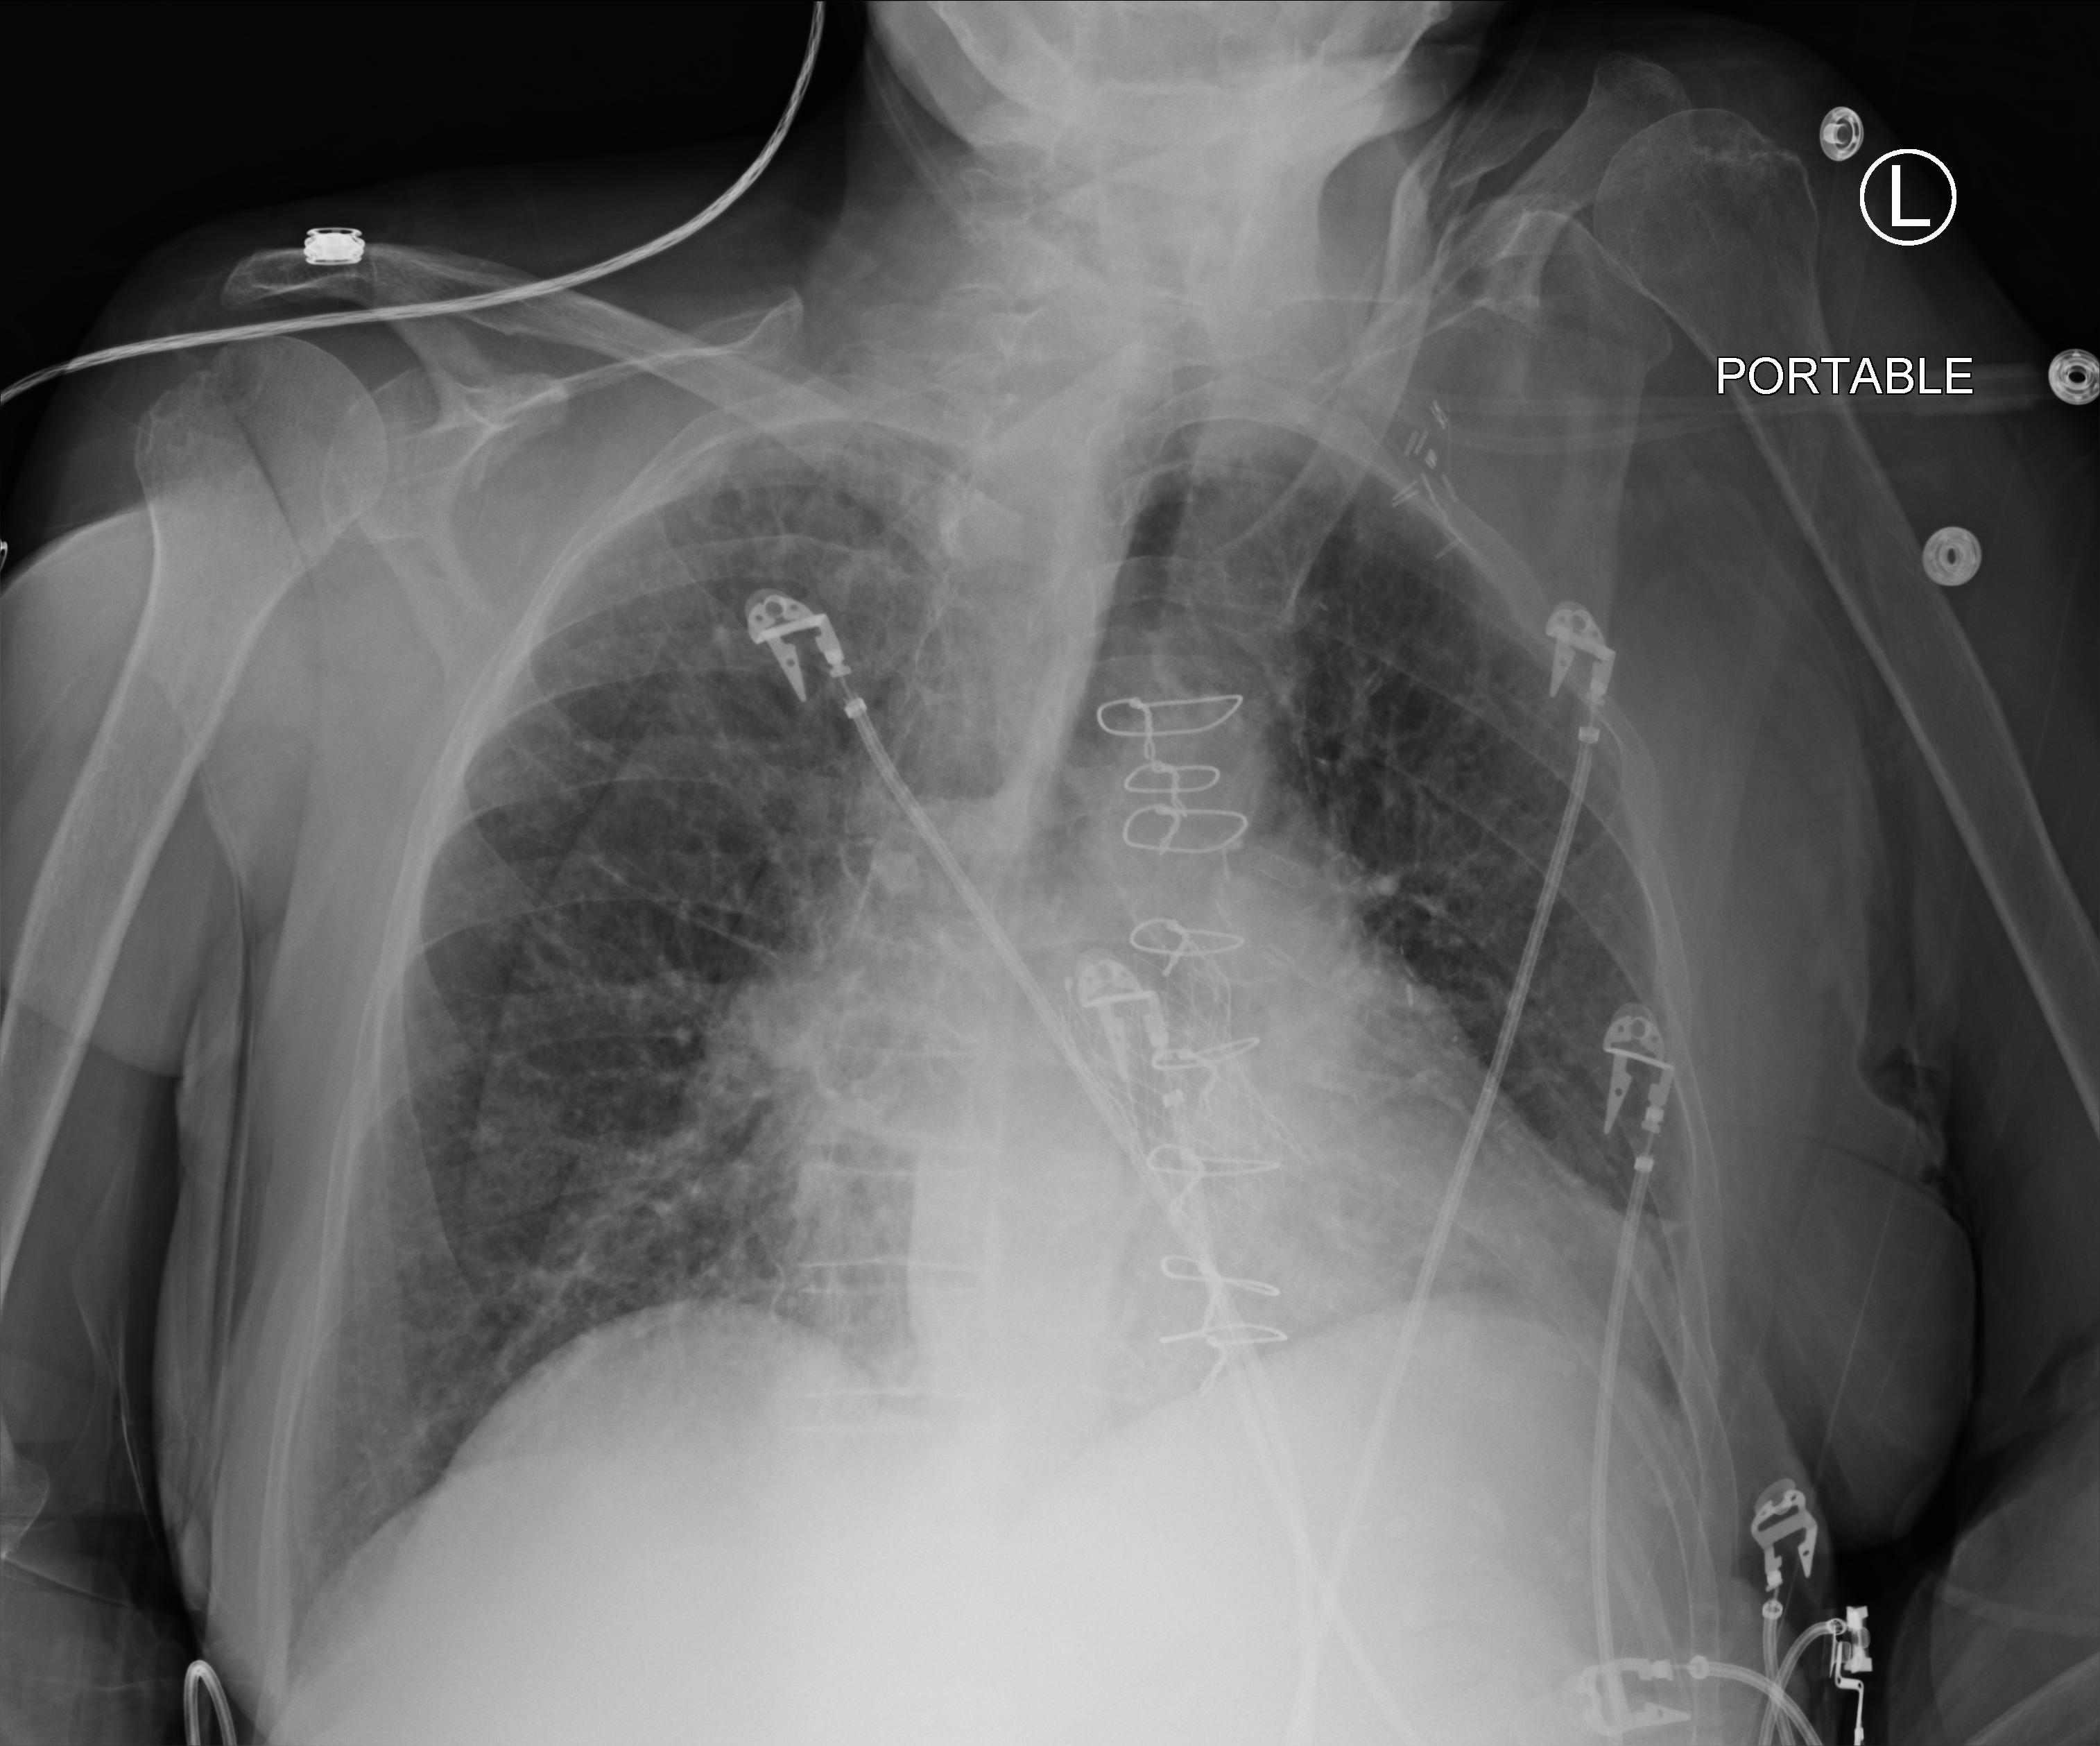
Chest X-ray (portable); anteroposterior (AP) projection. Female patient hospitalised with COVID-19, age 75–90 years.
From the hospital-stay record, not from the radiograph (when in the stay this image was taken is not recorded):
- length of hospital stay: 8 days
- admitted to intensive care during this hospital stay: yes
- mechanically ventilated during this hospital stay: no